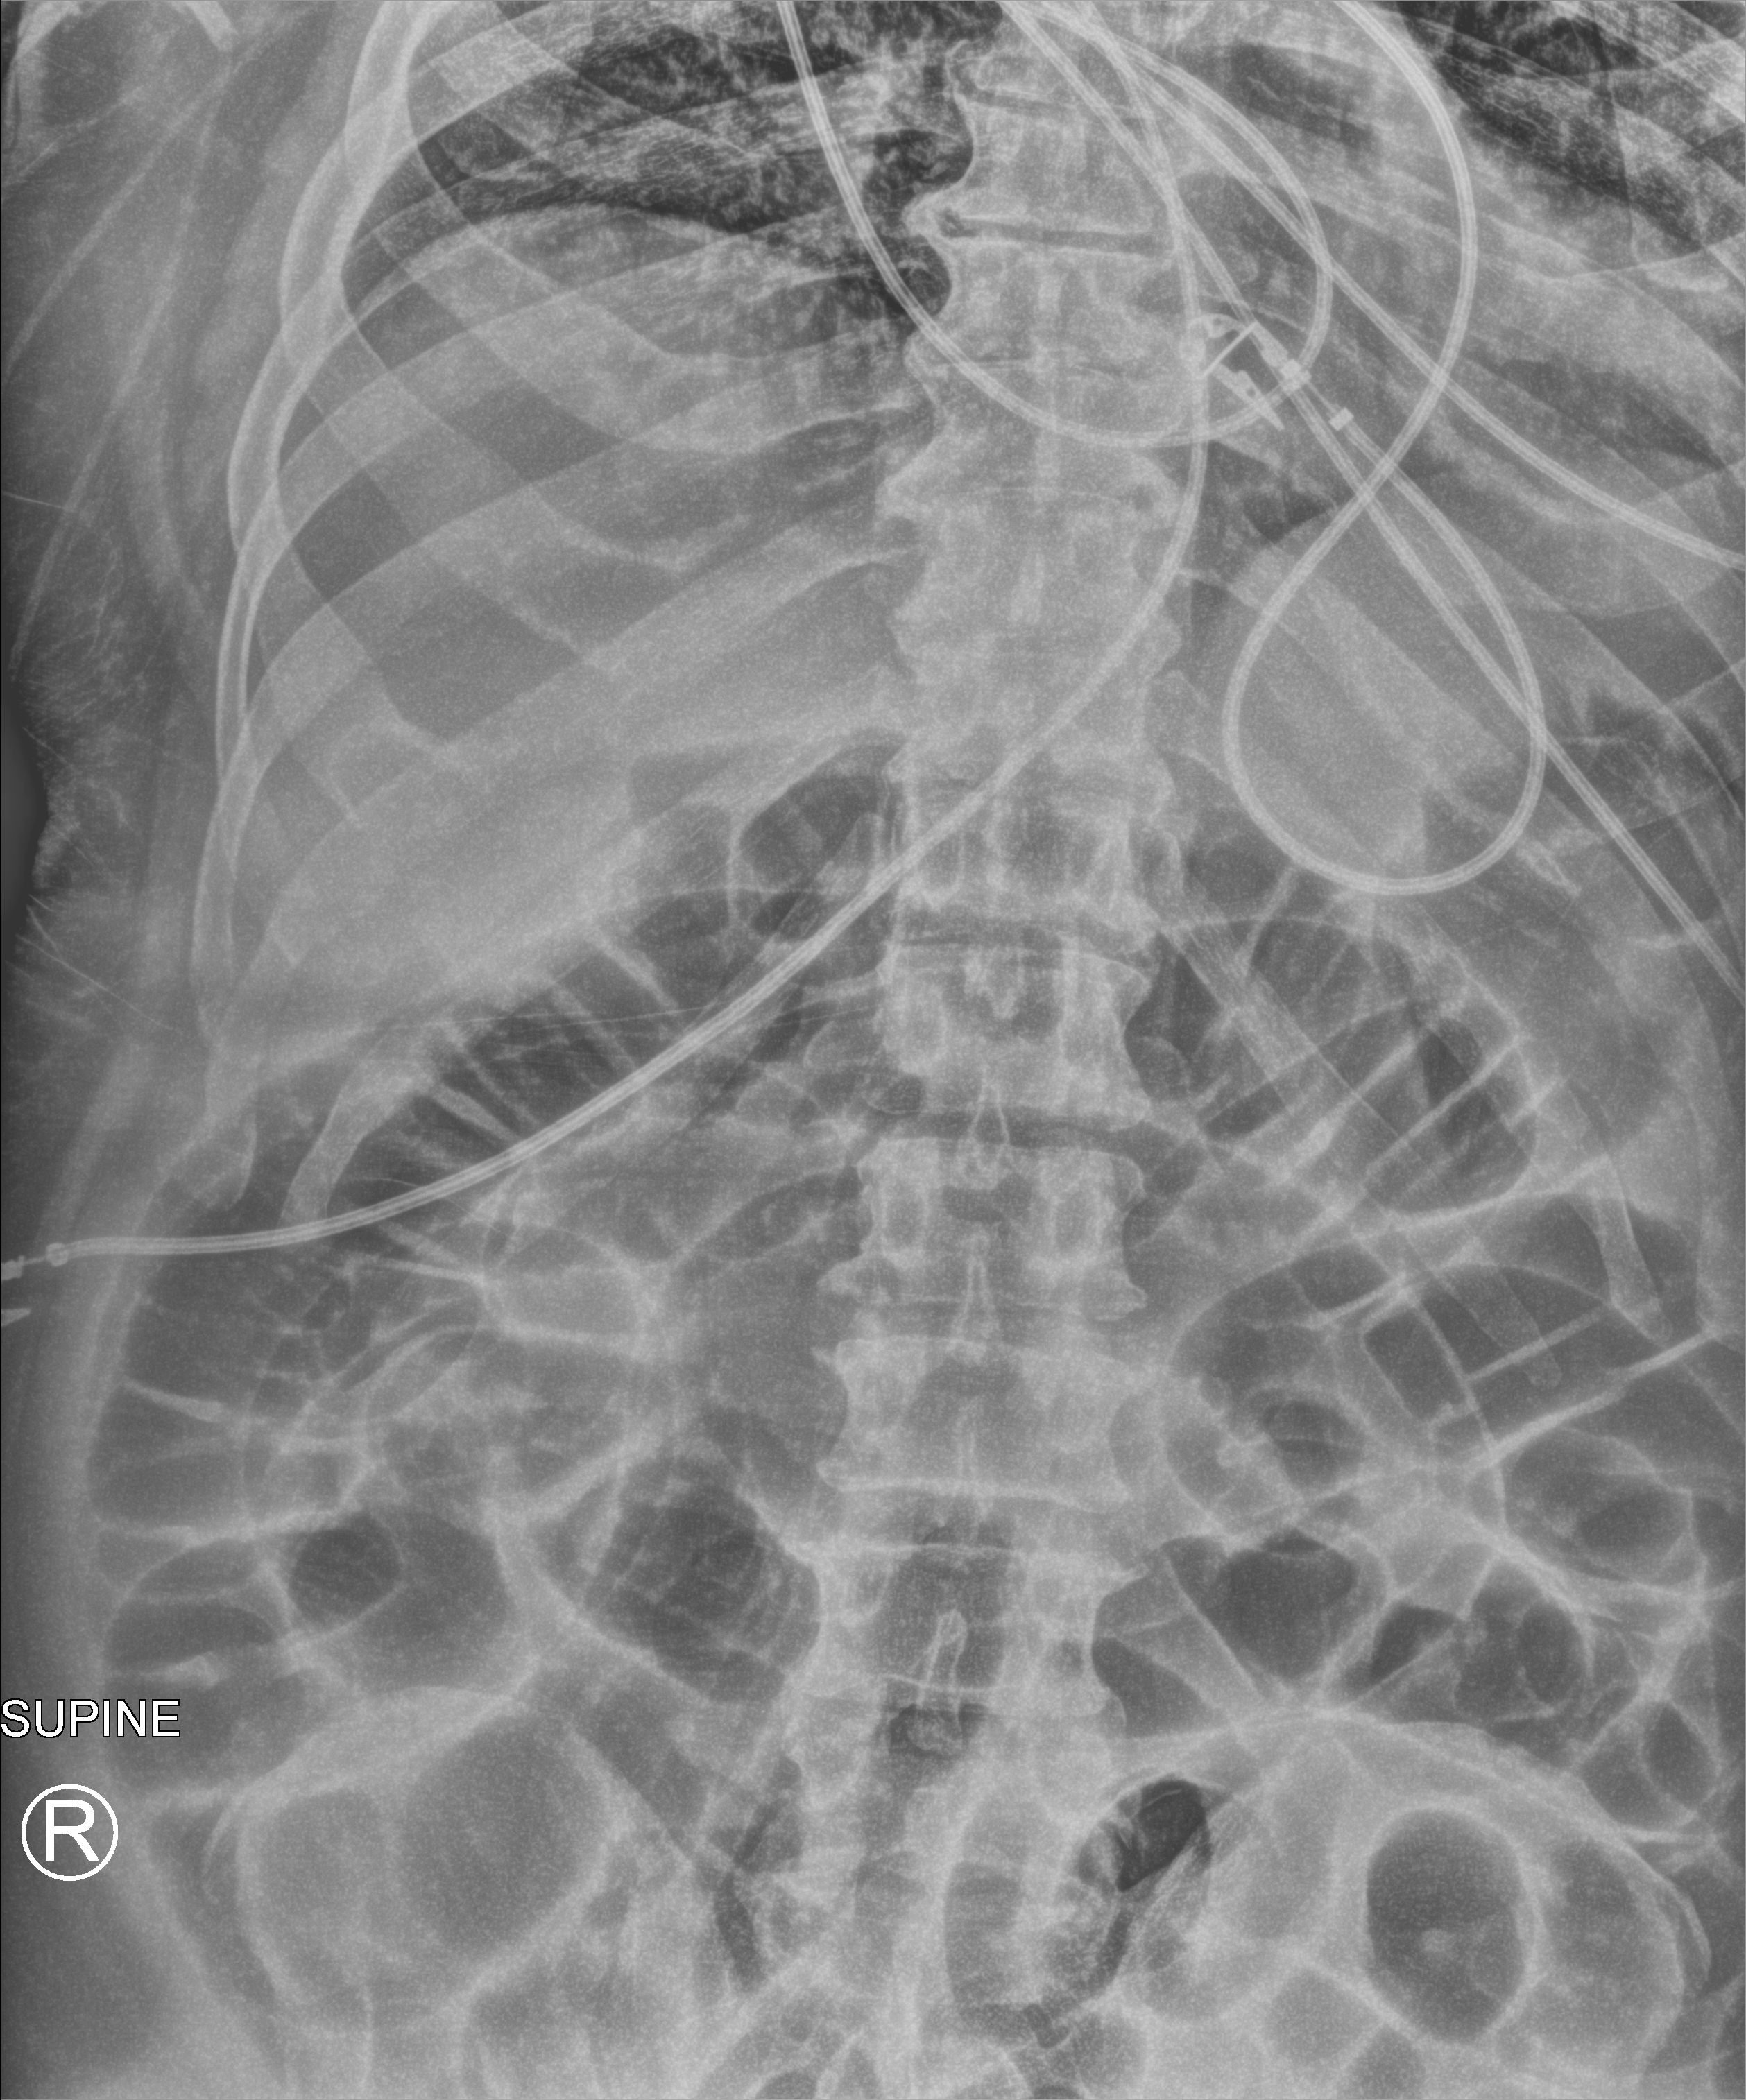
Abdomen X-ray (portable). Male patient hospitalised with COVID-19, age 18–59 years.
Hospital-stay facts (about this admission, not read from this image; timing relative to this image not recorded): smoking status (admission record): never; chronic kidney disease (admission record): no; mechanically ventilated during this hospital stay: yes.